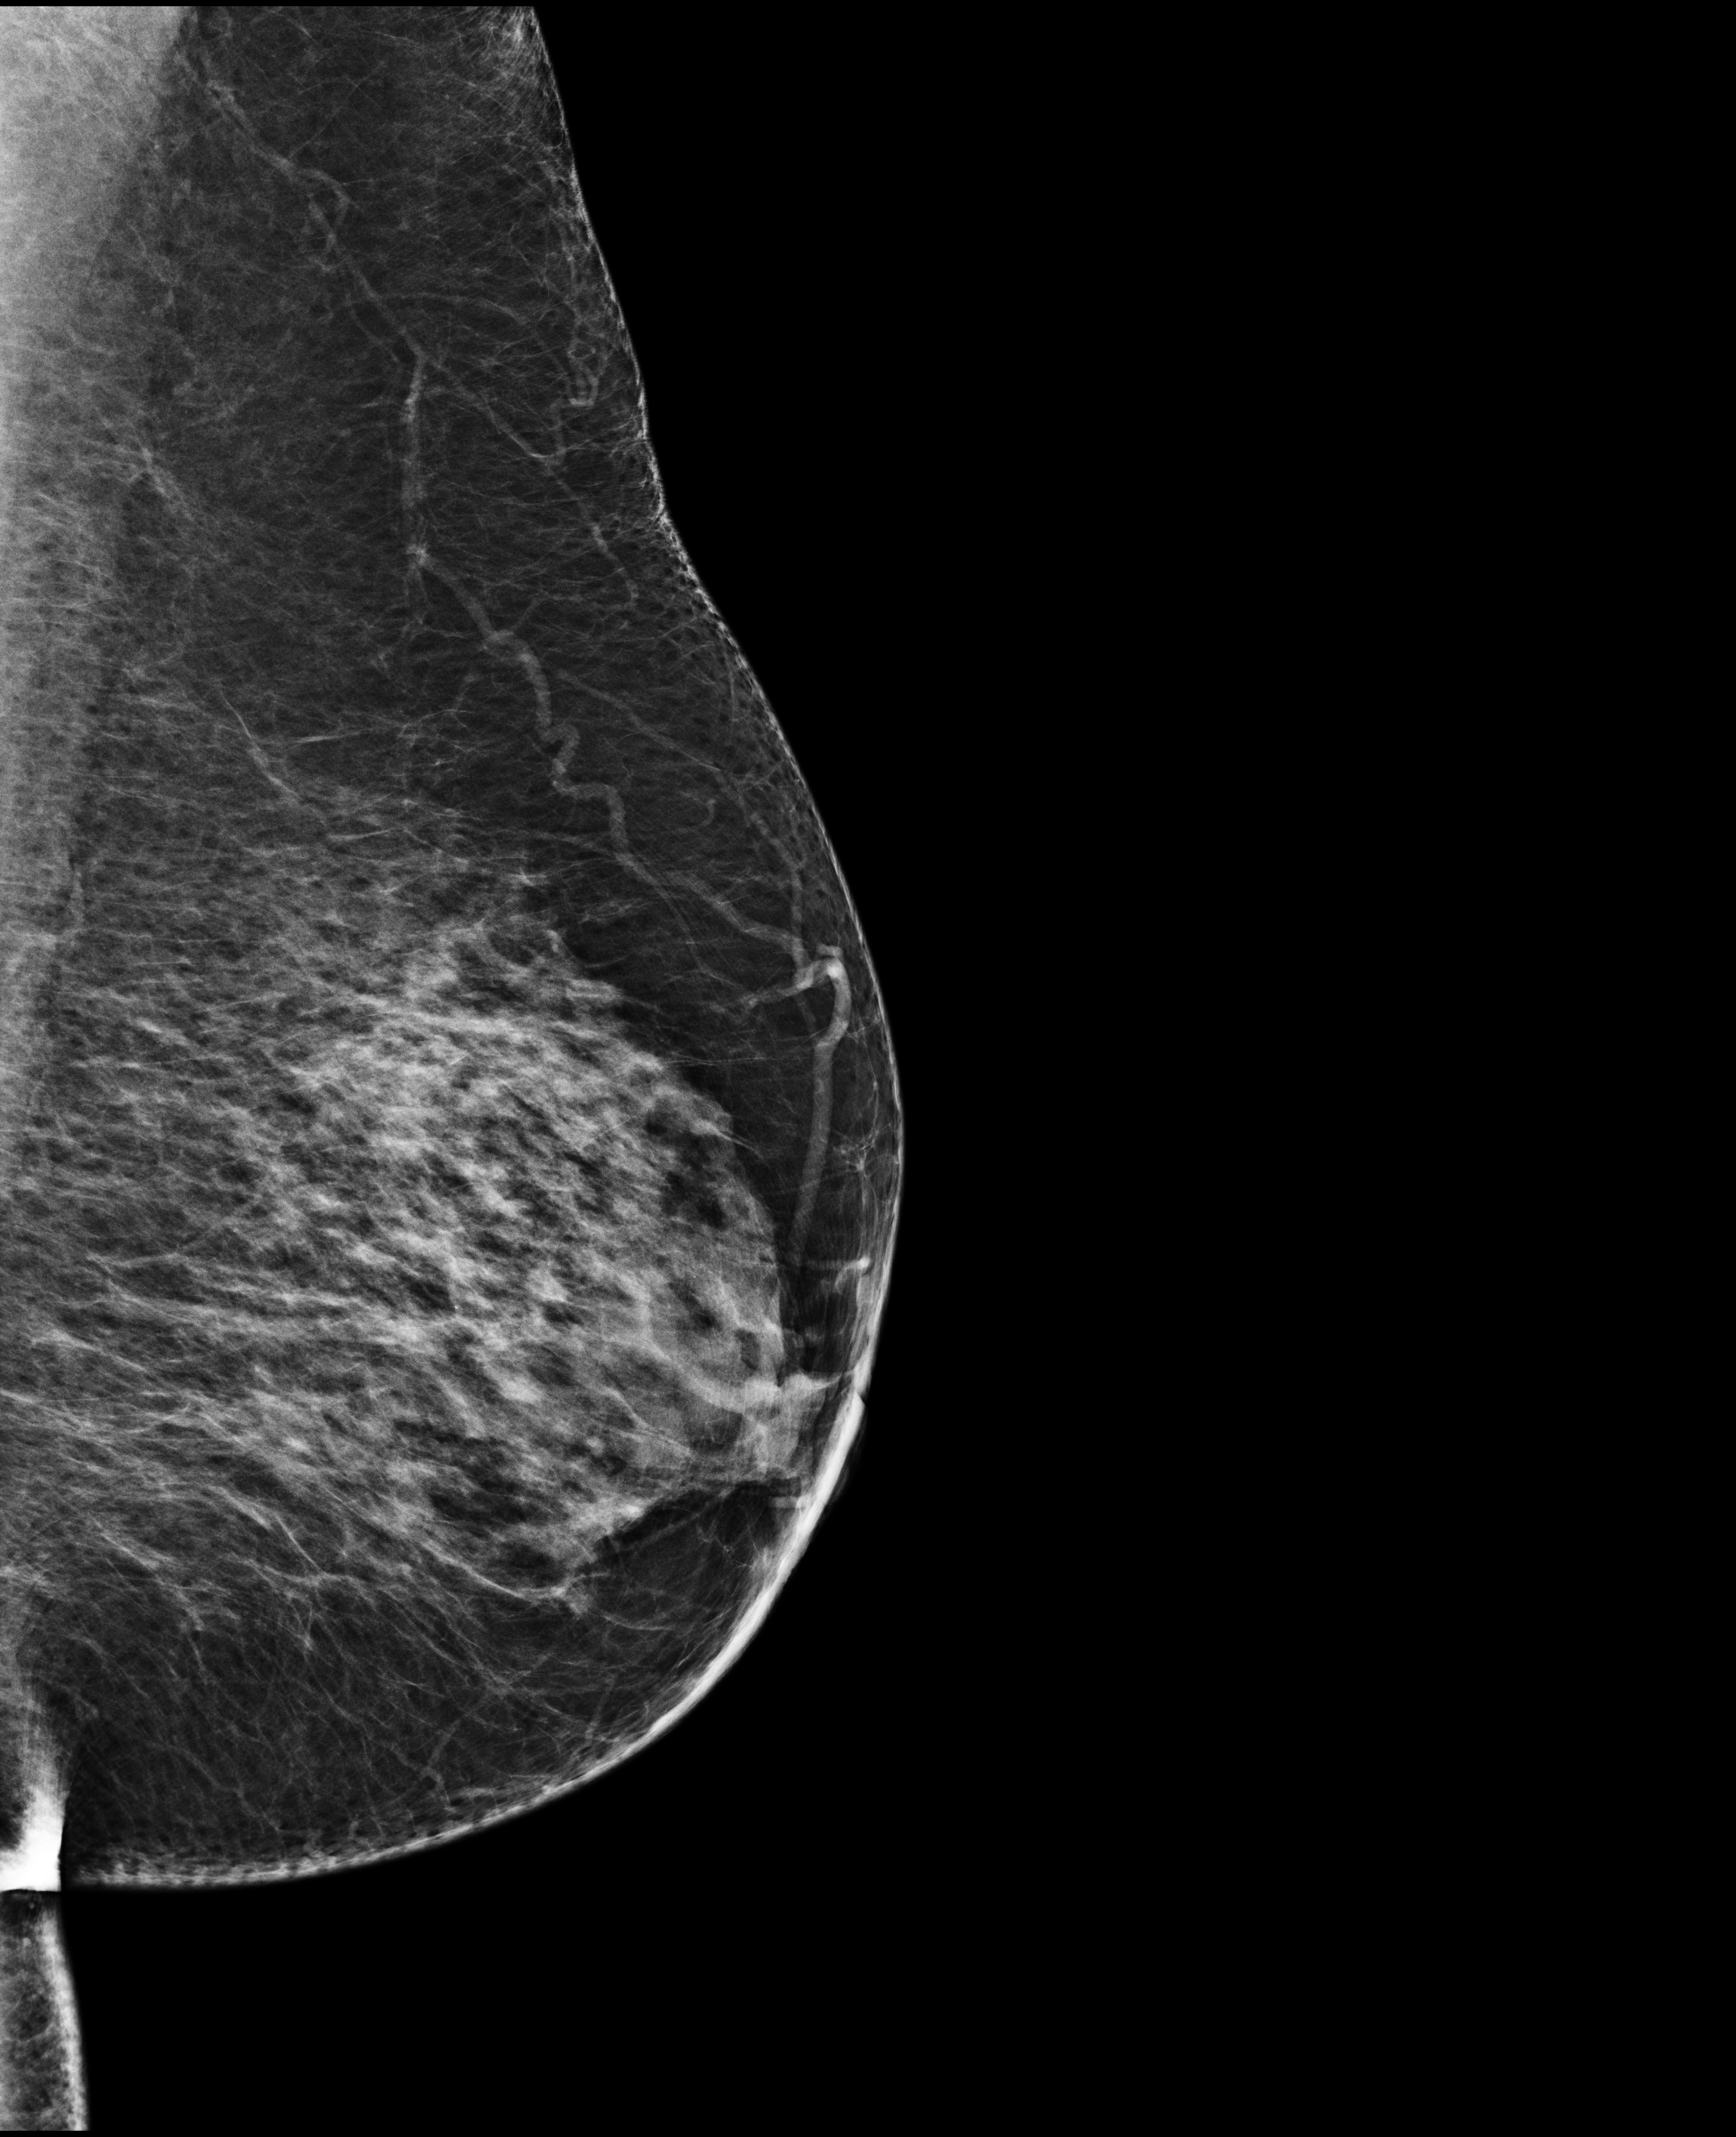
Annual screening mammography examination. Patient: female, 72 years.
Image type: full-field digital mammogram. Breast: left. Projection: MLO view.